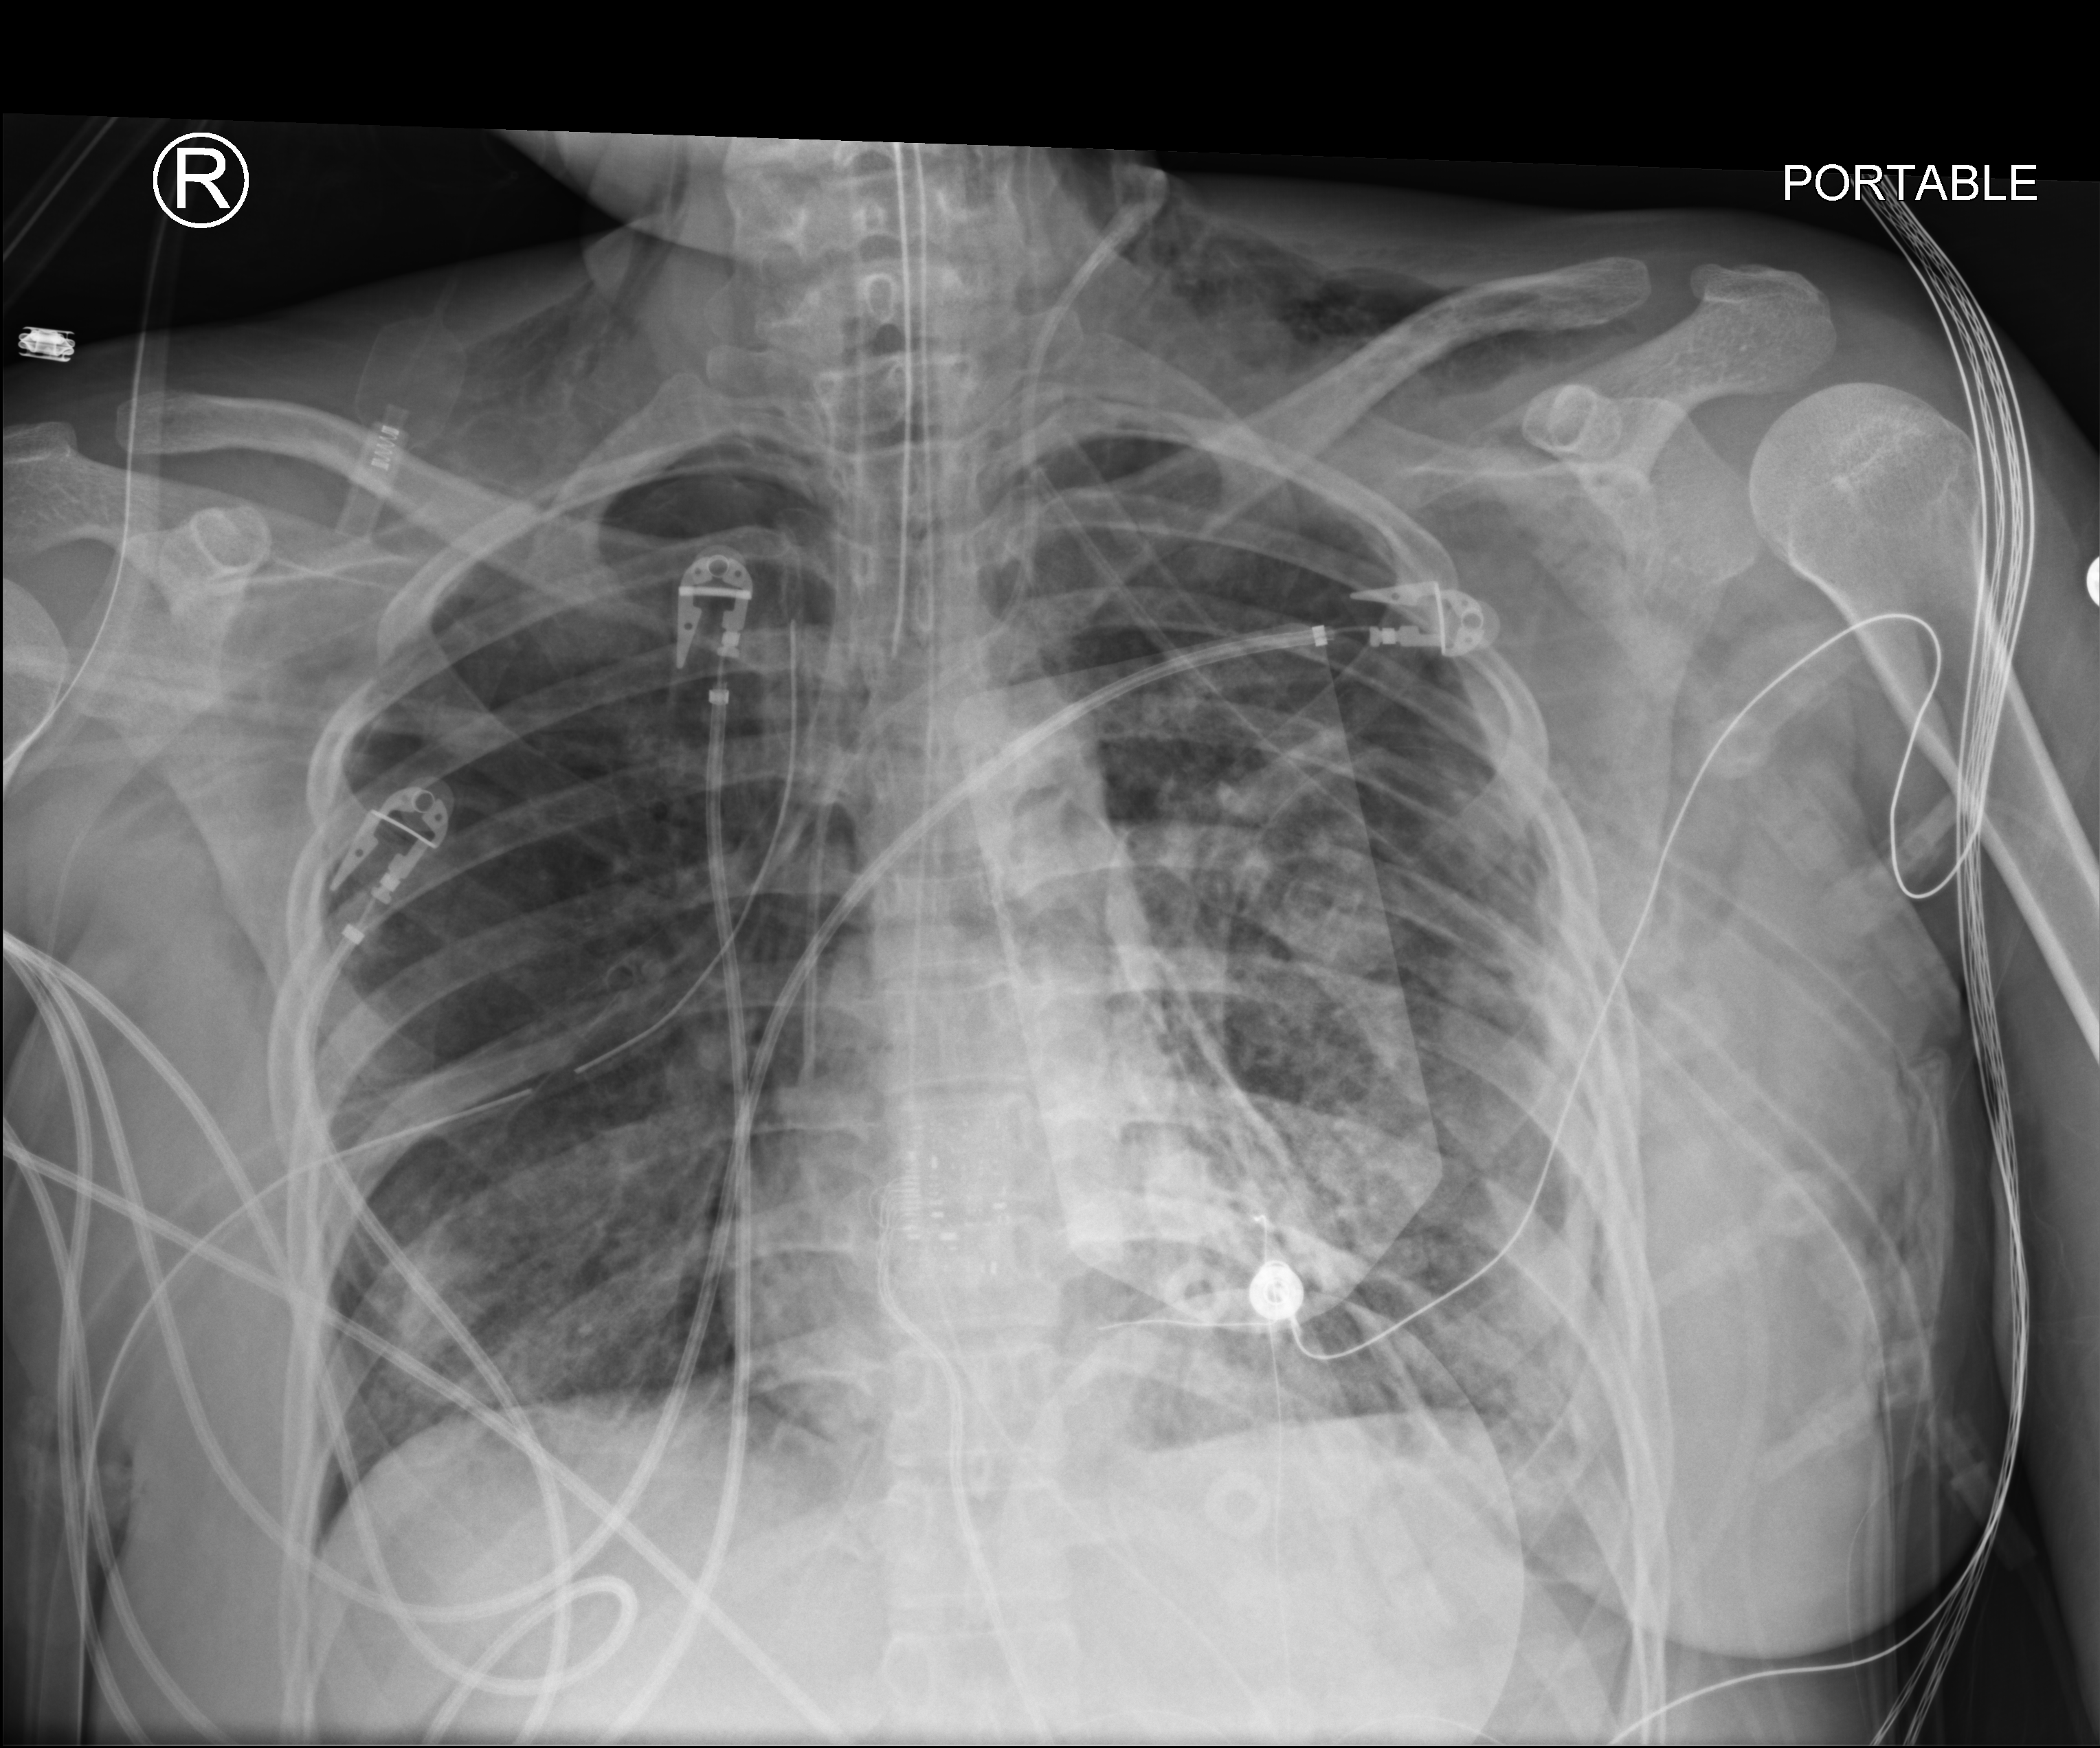
Bedside chest radiograph (computed radiography), anteroposterior (AP) projection. Patient hospitalised with COVID-19, aged 18–59 years.
Admission-level facts for this patient (not findings on this image; timing relative to this image not recorded): admitted to intensive care during this hospital stay: yes; mechanically ventilated during this hospital stay: yes; hypertension (admission record): no.